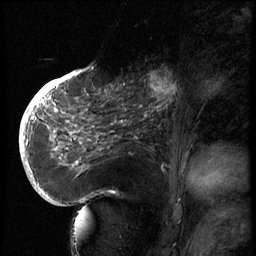
Breast MRI (dynamic contrast-enhanced), one sagittal slice; slice 31 of 66 in the series (ordered by position); 3 images stored at this slice position (order not interpretable as contrast timing); 1.5 T; TE 4.2 ms, TR 8.9 ms; 2.5 mm slice thickness; 256 × 256 image matrix, field of view 200 × 200 mm. Patient: female, 56 years. From the clinical record (not read from this slice): setting: breast cancer imaged before/during neoadjuvant chemotherapy.
Annotated regions visible in this slice (semi-automatically segmented with operator editing):
- analysis volume of interest (the breast-tissue region the enhancement analysis was run in; not a lesion): bounding box <129,62,194,127> (left, top, right, bottom; pixels)
- tumour enhancement mask (voxels above the 140 % enhancement threshold inside the analysis volume of interest): <145,70,183,118>